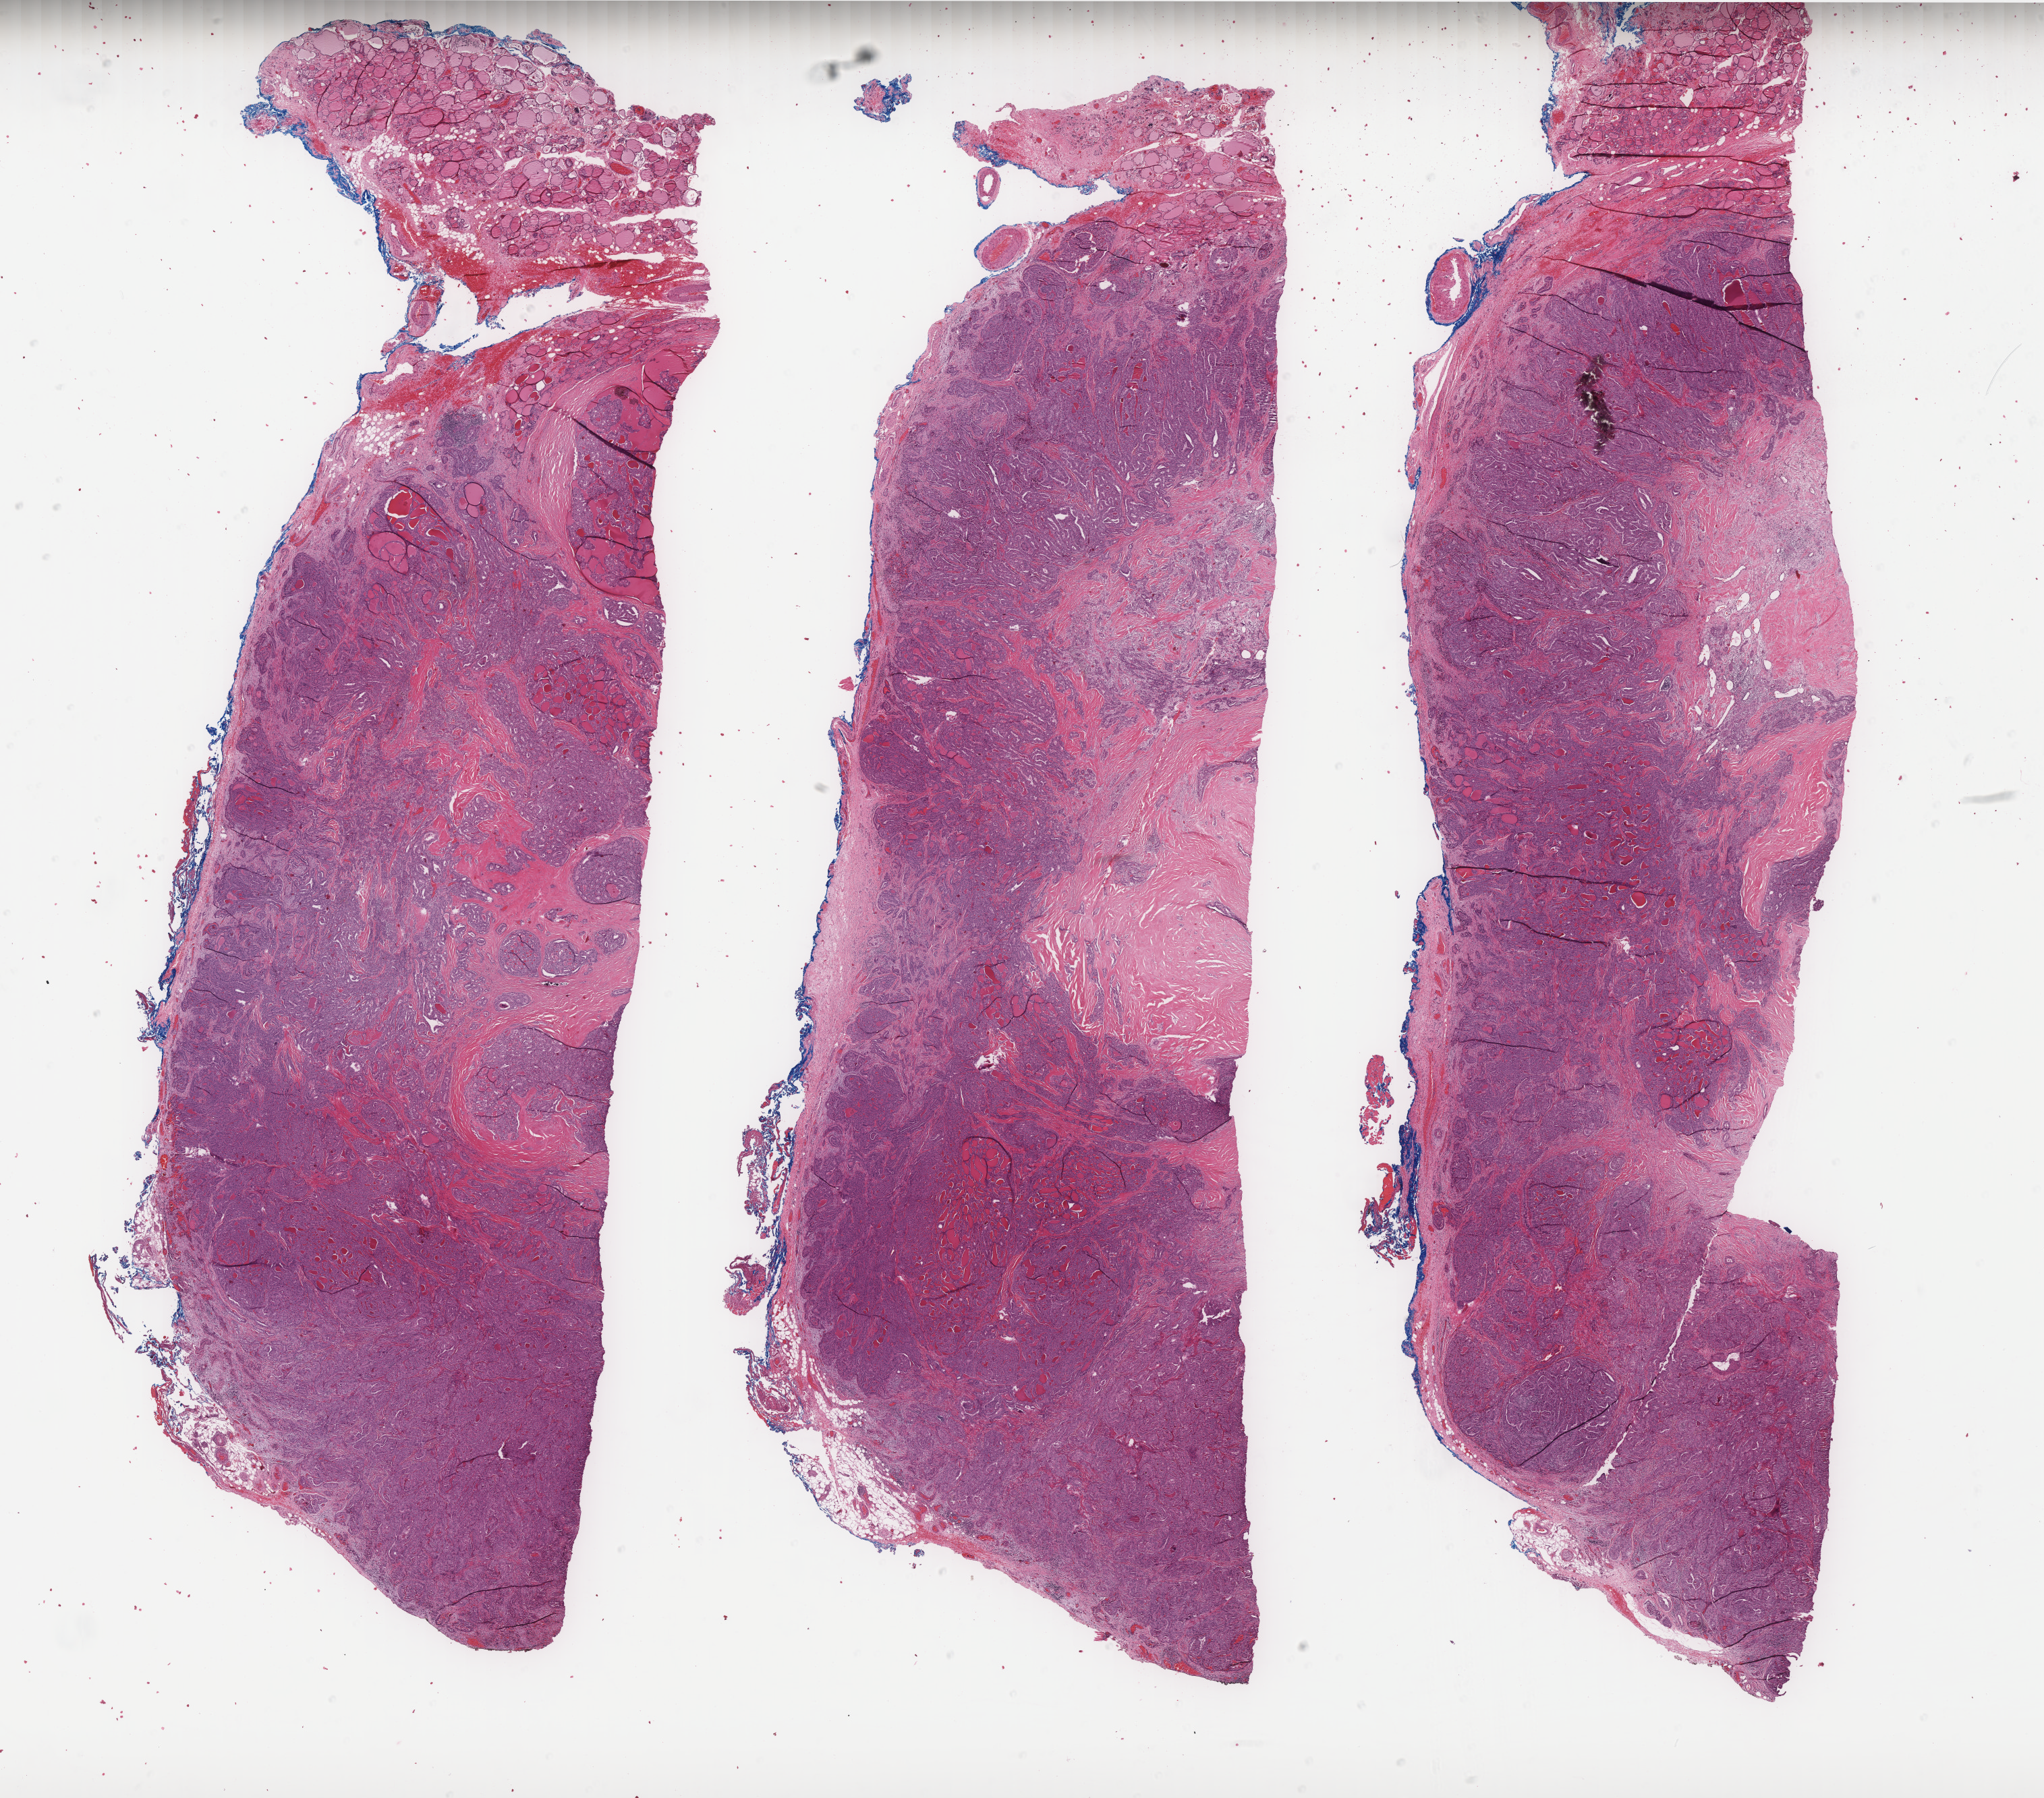
Whole-slide histology image, H&E — shown as a low-resolution overview of the whole scanned area (about 24.3 x 21.4 mm, slide scanned at 40x); formalin-fixed paraffin-embedded (FFPE) diagnostic section; primary tumour sample from the thyroid. Patient: male, age at initial diagnosis 66 years.
Diagnosis: Papillary adenocarcinoma, NOS (thyroid gland). AJCC pathologic stage: IVA. Lymph nodes positive (case pathology): 5 of 6 examined. Laterality: right.